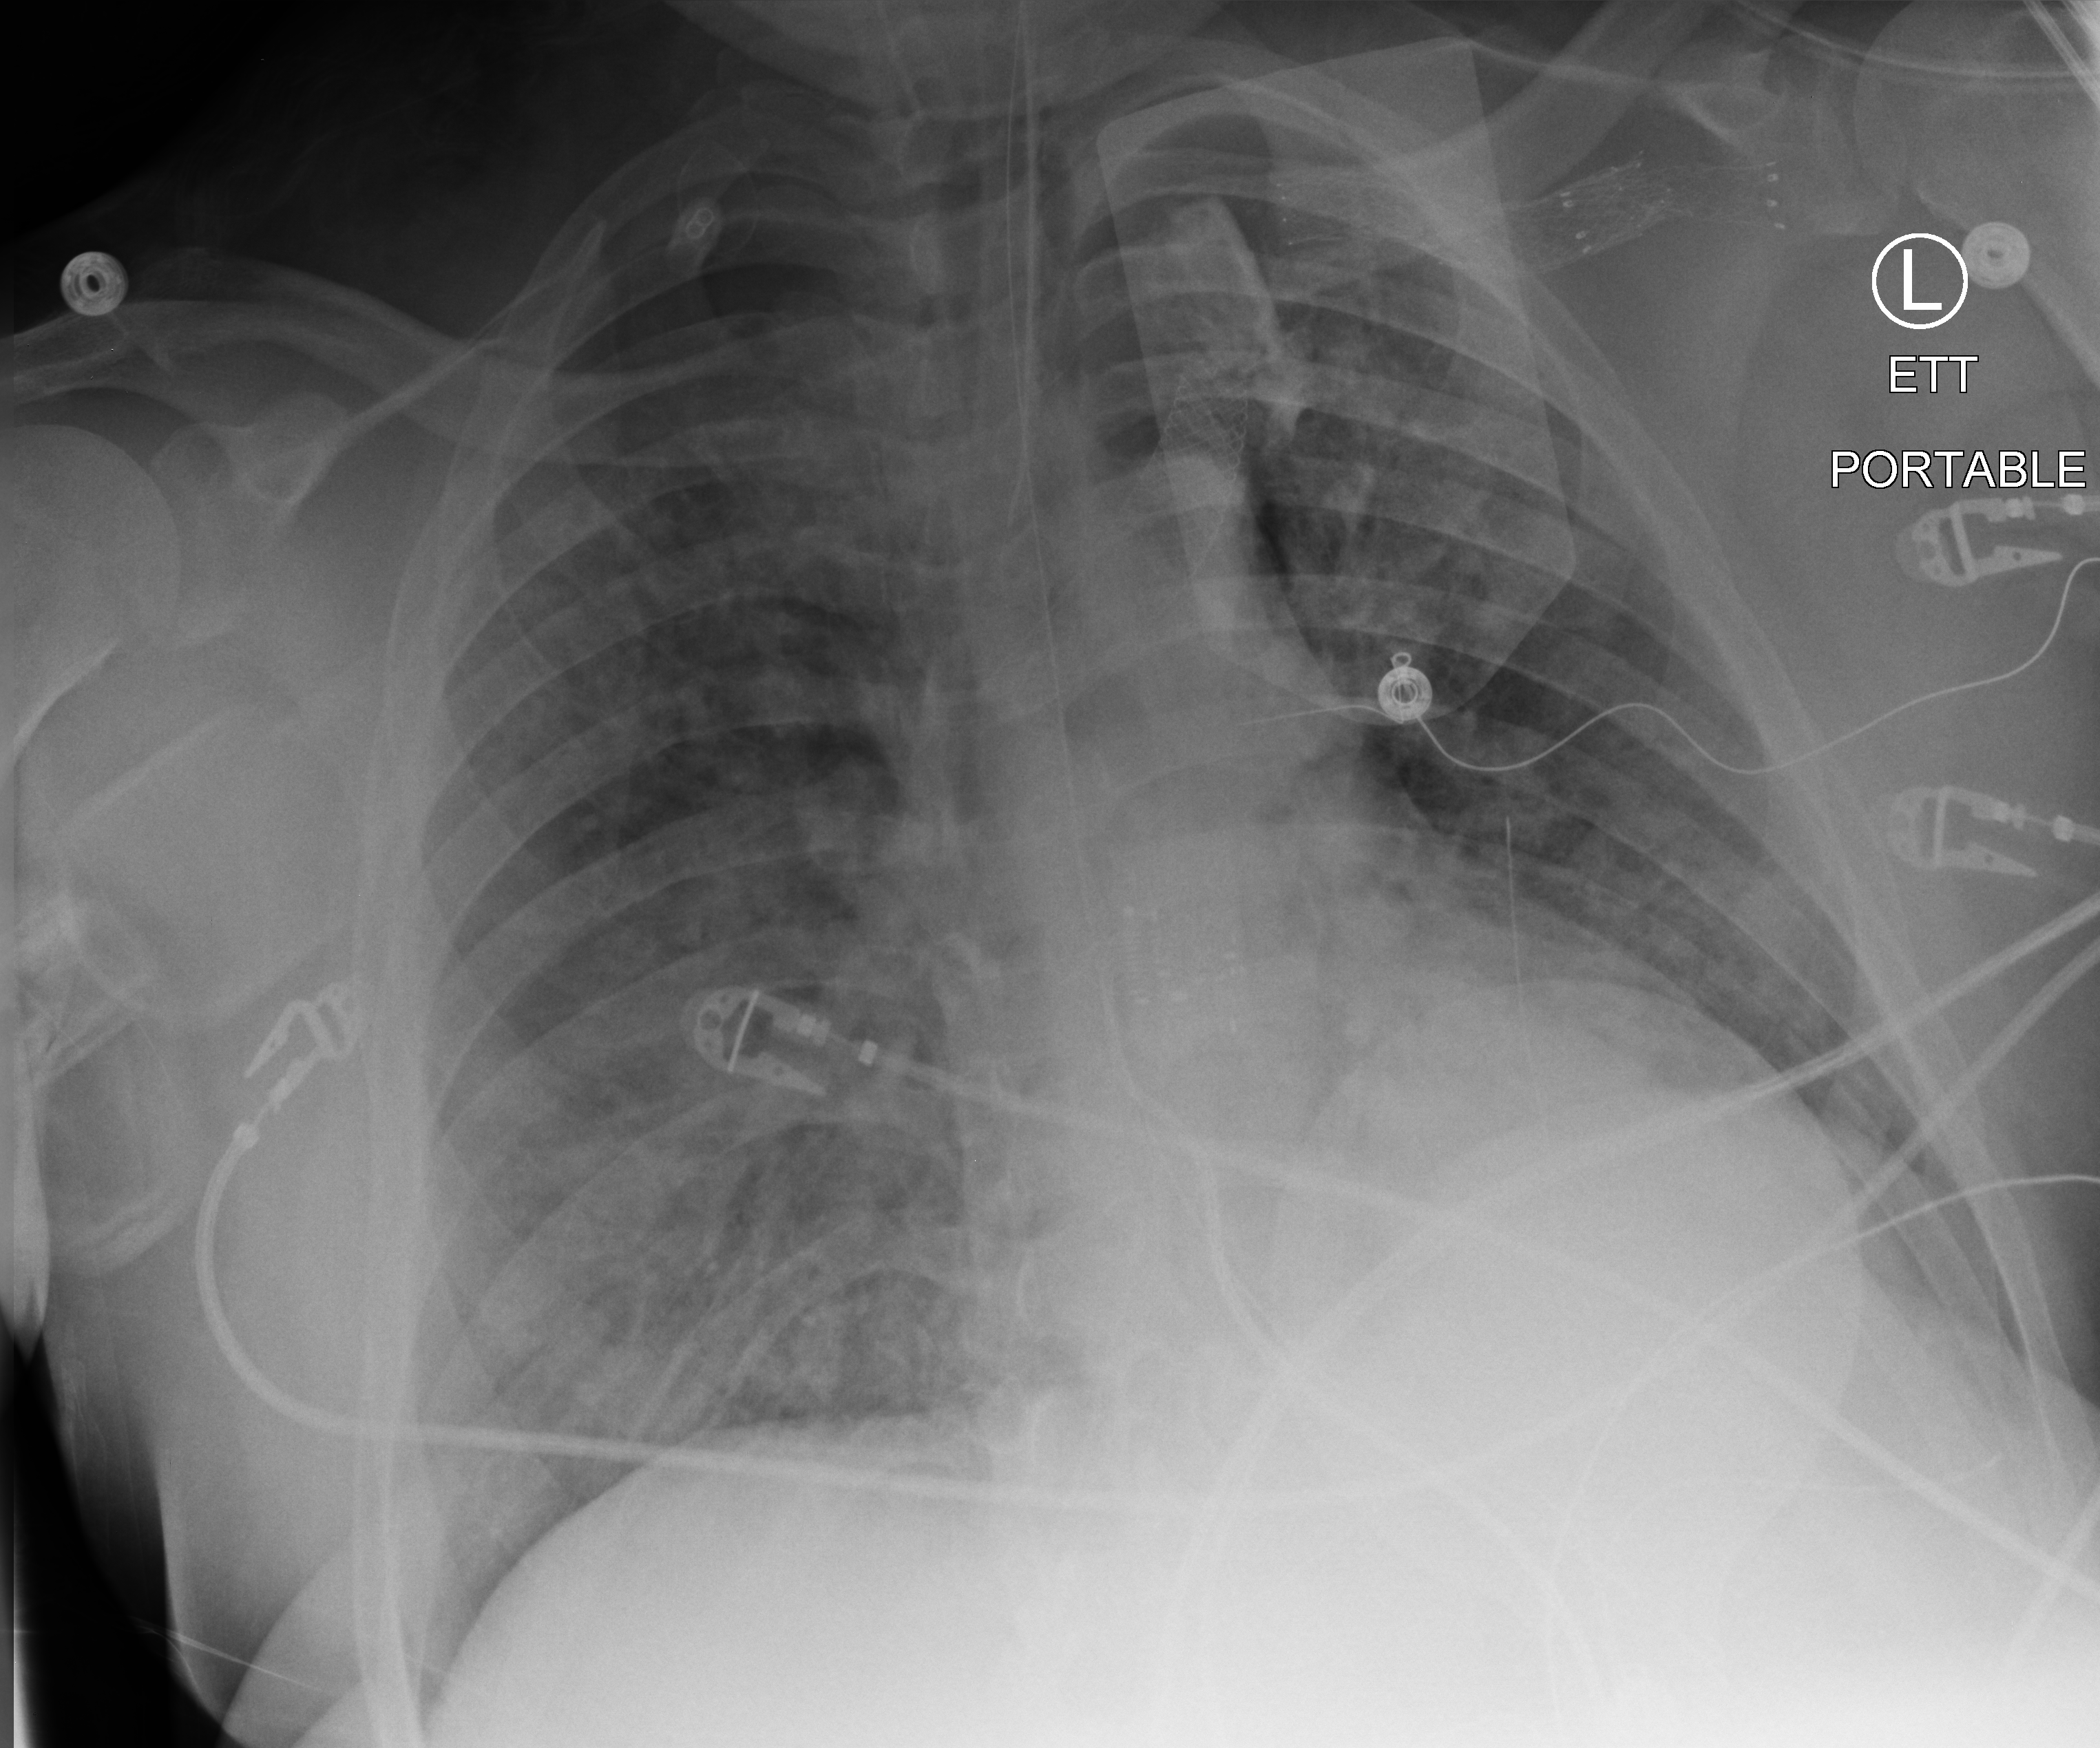
Bedside chest radiograph (computed radiography); anteroposterior (AP) projection. Male patient hospitalised with COVID-19, age 18–59 years.
From the hospital-stay record, not from the radiograph (when in the stay this image was taken is not recorded):
- length of hospital stay: 41 days
- mechanically ventilated during this hospital stay: yes
- diabetes (admission record): no